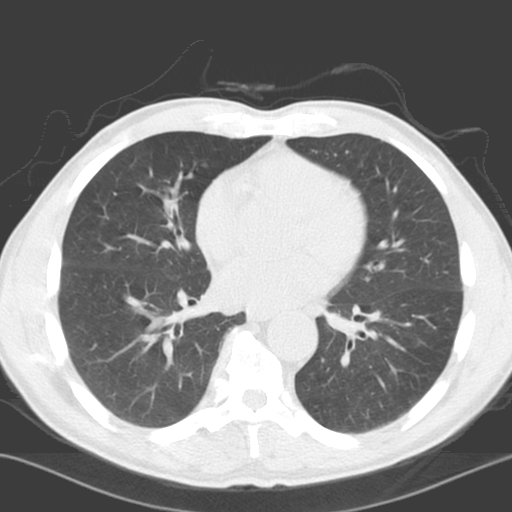
Low-dose screening chest CT, axial slice, first (baseline) screen, lung window (W 1500 / L -600 HU), 3.2 mm slice thickness, slice 101 of 178 in the series. Male participant, aged 65 years at enrolment. Current smoker at enrolment.
Expert reader's lesion annotation, bounding box [x1, y1, x2, y2] px = [138, 162, 201, 225]. Screening reader's record for this exam (one nodule recorded; not confirmed to be the boxed lesion): non-calcified nodule or mass ≥4 mm, right lower lobe, 5 × 5 mm, poorly defined margins, soft tissue attenuation. Participant outcome: lung cancer diagnosed 1144 days after this screen (after the third annual screen) — squamous cell carcinoma, NOS, right middle lobe, poorly differentiated (G3), stage IA (AJCC 6th edition), 23 mm at pathology.